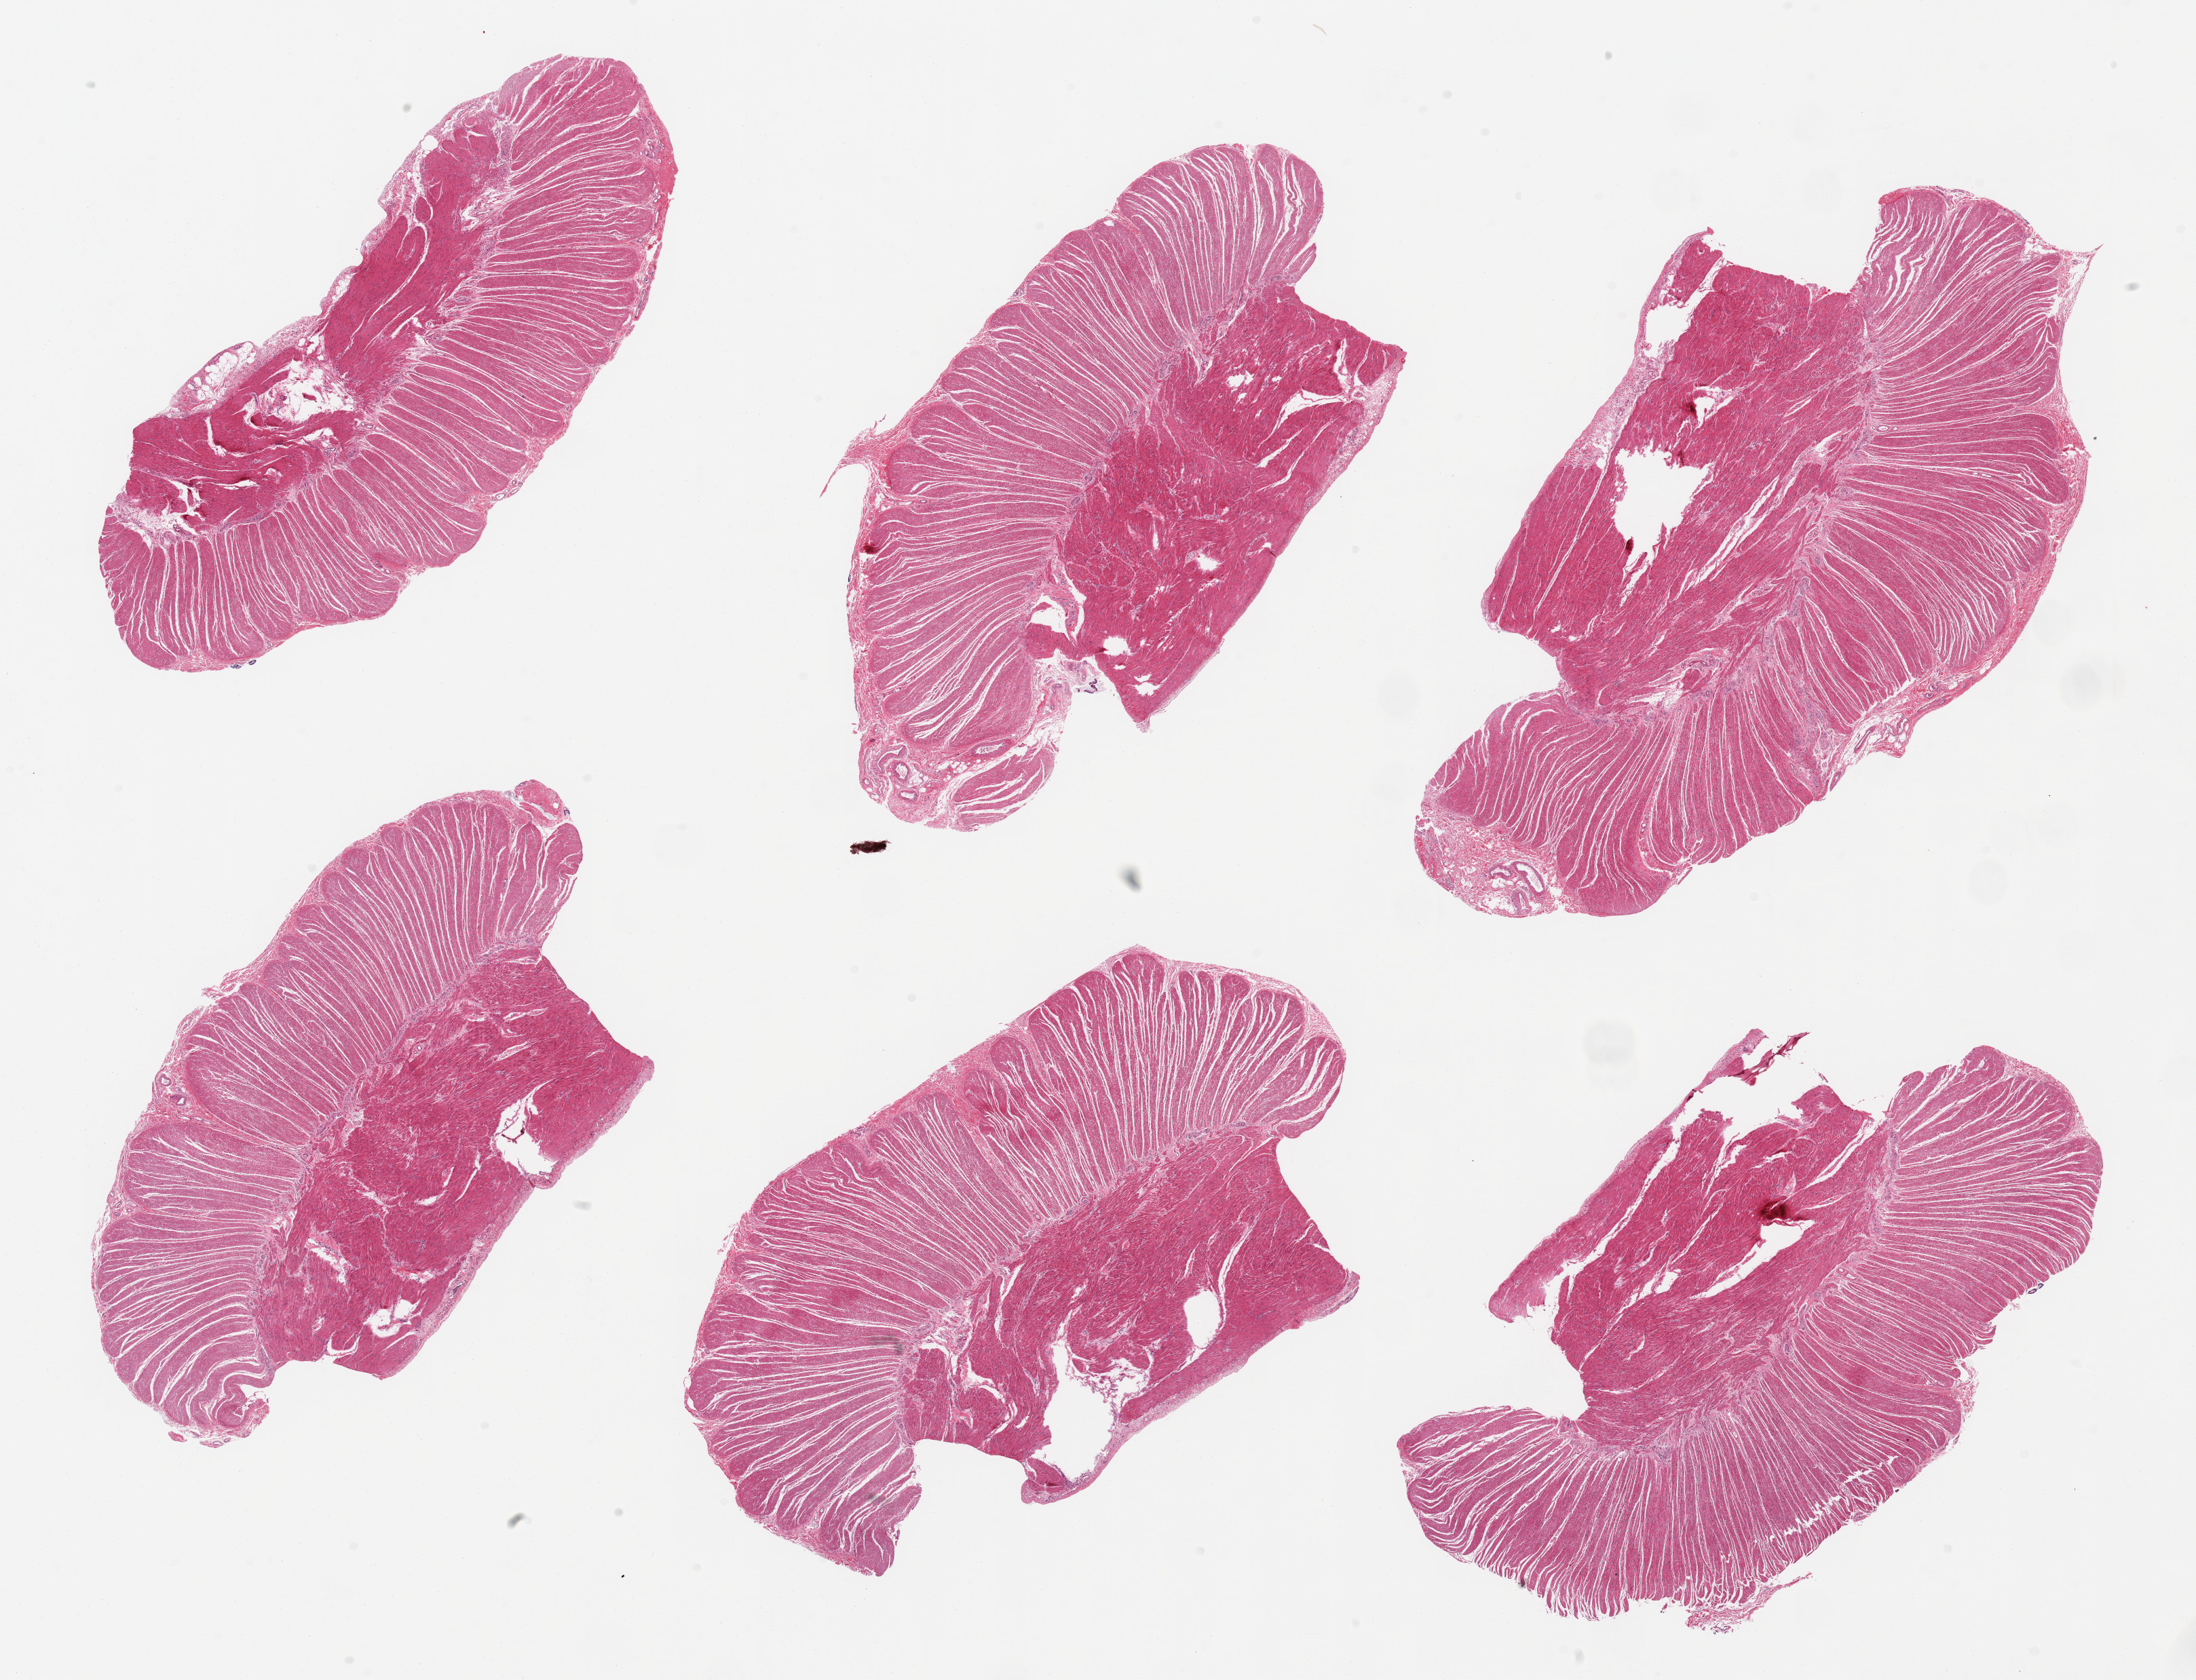
H&E whole-slide image — whole scanned area (about 25.6 x 19.6 mm, acquisition: 20x scan) shown as a low-resolution overview. PAXgene-fixed, paraffin-embedded tissue. Sampled site (target tissue): sigmoid colon. Donor tissue sample. Male donor.
Review note (as recorded): 6 pieces, confirmed target muscularis.